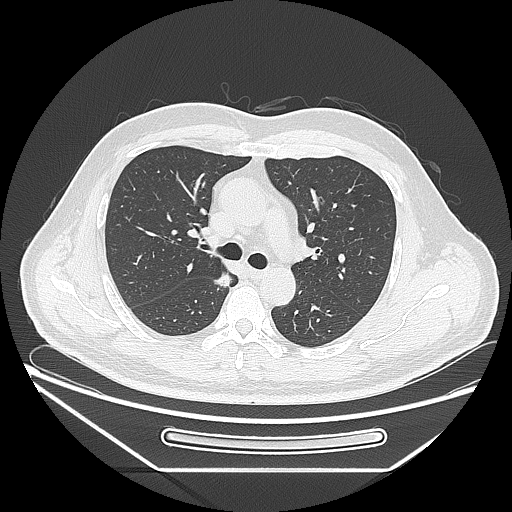
Chest CT, one axial slice; position 165 of 271 along the scan axis; lung window (W 1500 / L -600 HU); 1.25 mm slice thickness; 512 × 512 image matrix, field of view 414 × 414 mm. Patient: male, 49 years. Case-level facts recorded for this patient, not image findings: clinical TNM (as recorded): T1b N0 M0; histopathological grade: G2.
Structures marked on this image (rectangle marked by the reading radiologist):
- lung tumour (recorded histology: adenocarcinoma): bounding box (x1, y1, x2, y2) in pixels: (213, 270, 232, 295)